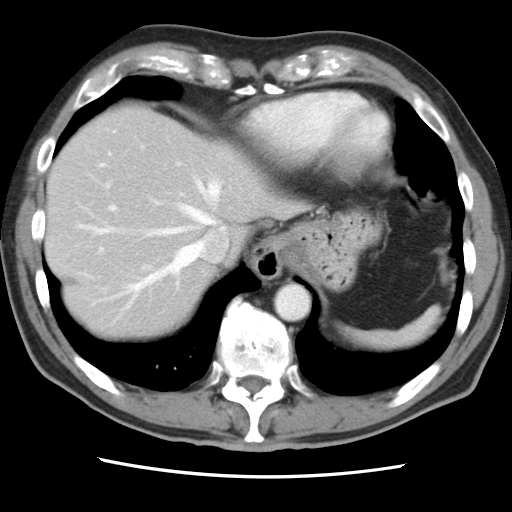
Contrast-enhanced abdominal CT, one axial slice; slice 70 of 83 in the series (ordered by position); 120 kVp; intravenous contrast given; soft-tissue window (W 400 / L 40 HU); 512 × 512 image matrix. Male patient, age 69 years. Case-level facts recorded for this patient, not image findings: diagnosis: colorectal cancer liver metastases, imaged before liver resection; multiple liver metastases: yes; largest metastasis: 3.5 cm; disease in both lobes: no.
Annotated regions visible in this slice (manually delineated by an expert):
- hepatic veins: bounding box <83,131,226,307> (left, top, right, bottom; pixels)
- liver: <46,108,296,340>
- planned liver remnant (the part of the liver to remain after resection): <46,148,214,340>
- portal vein (with intrahepatic branches): <99,184,184,269>